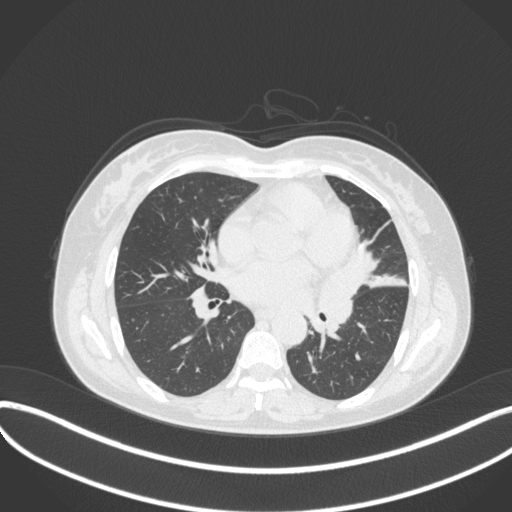
Chest CT, one axial slice; position 171 of 373 along the scan axis; reconstruction kernel B31f; 120 kVp; lung window (W 1500 / L -600 HU); 1 mm slice thickness; 512 × 512 image matrix, field of view 400 × 400 mm. Female patient, age 54 years. From the clinical record (not read from this slice): clinical TNM (as recorded): T2a N1 M0; histopathological grade: G3.
Structures marked on this image (bounding box drawn by a radiologist):
- lung tumour (recorded histology: small cell carcinoma): bounding box [x1, y1, x2, y2] px = [312, 256, 369, 332]